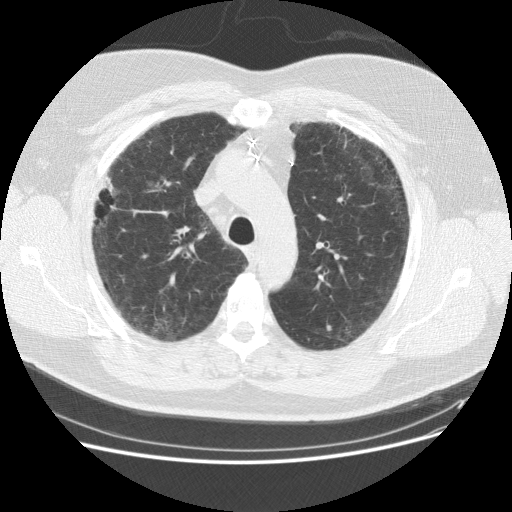
Low-dose screening chest CT, one axial slice; position 116 of 151 along the scan axis; reconstruction kernel STANDARD; lung window (W 1500 / L -600 HU); 512 × 512 image matrix.
Structures marked on this image (expert manual segmentation):
- lesion 2 (tumor, upper lobe of right lung): bounding box [x1, y1, x2, y2] px = [99, 178, 116, 195]